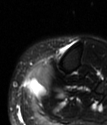
MRI of an extremity soft-tissue mass, one axial slice. Slice 20 of 78 in the series (ordered by position). T2-weighted fat-saturated. MR volume resampled by the dataset authors to the PET/CT grid (not the native acquisition matrix). 3.27 mm slice thickness. 107 × 125 image matrix, field of view 104 × 122 mm. Female patient. Case-level facts recorded for this patient, not image findings: histological type: extraskeletal high grade osteogenic sarcoma; grade: high; site of the primary tumour: left calf.
Outlined on this slice (expert contour drawn on MRI and transferred to this co-registered scan by the dataset authors):
- gross tumour volume (mass): bounding box [x1, y1, x2, y2] px = [26, 65, 52, 94]